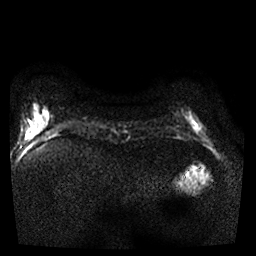
Breast MRI, one axial slice. Slice 3 of 25 in the series (ordered by position). Diffusion-weighted series; image 2 of 4 stored at this slice position (different b-values; order by instance number). 1.5 T. 4 mm slice thickness. 256 × 256 image matrix. Female patient.
Outlined on this slice (outlined manually by an expert reader):
- tumour on diffusion-weighted imaging: bounding box <188,118,198,128> (left, top, right, bottom; pixels)